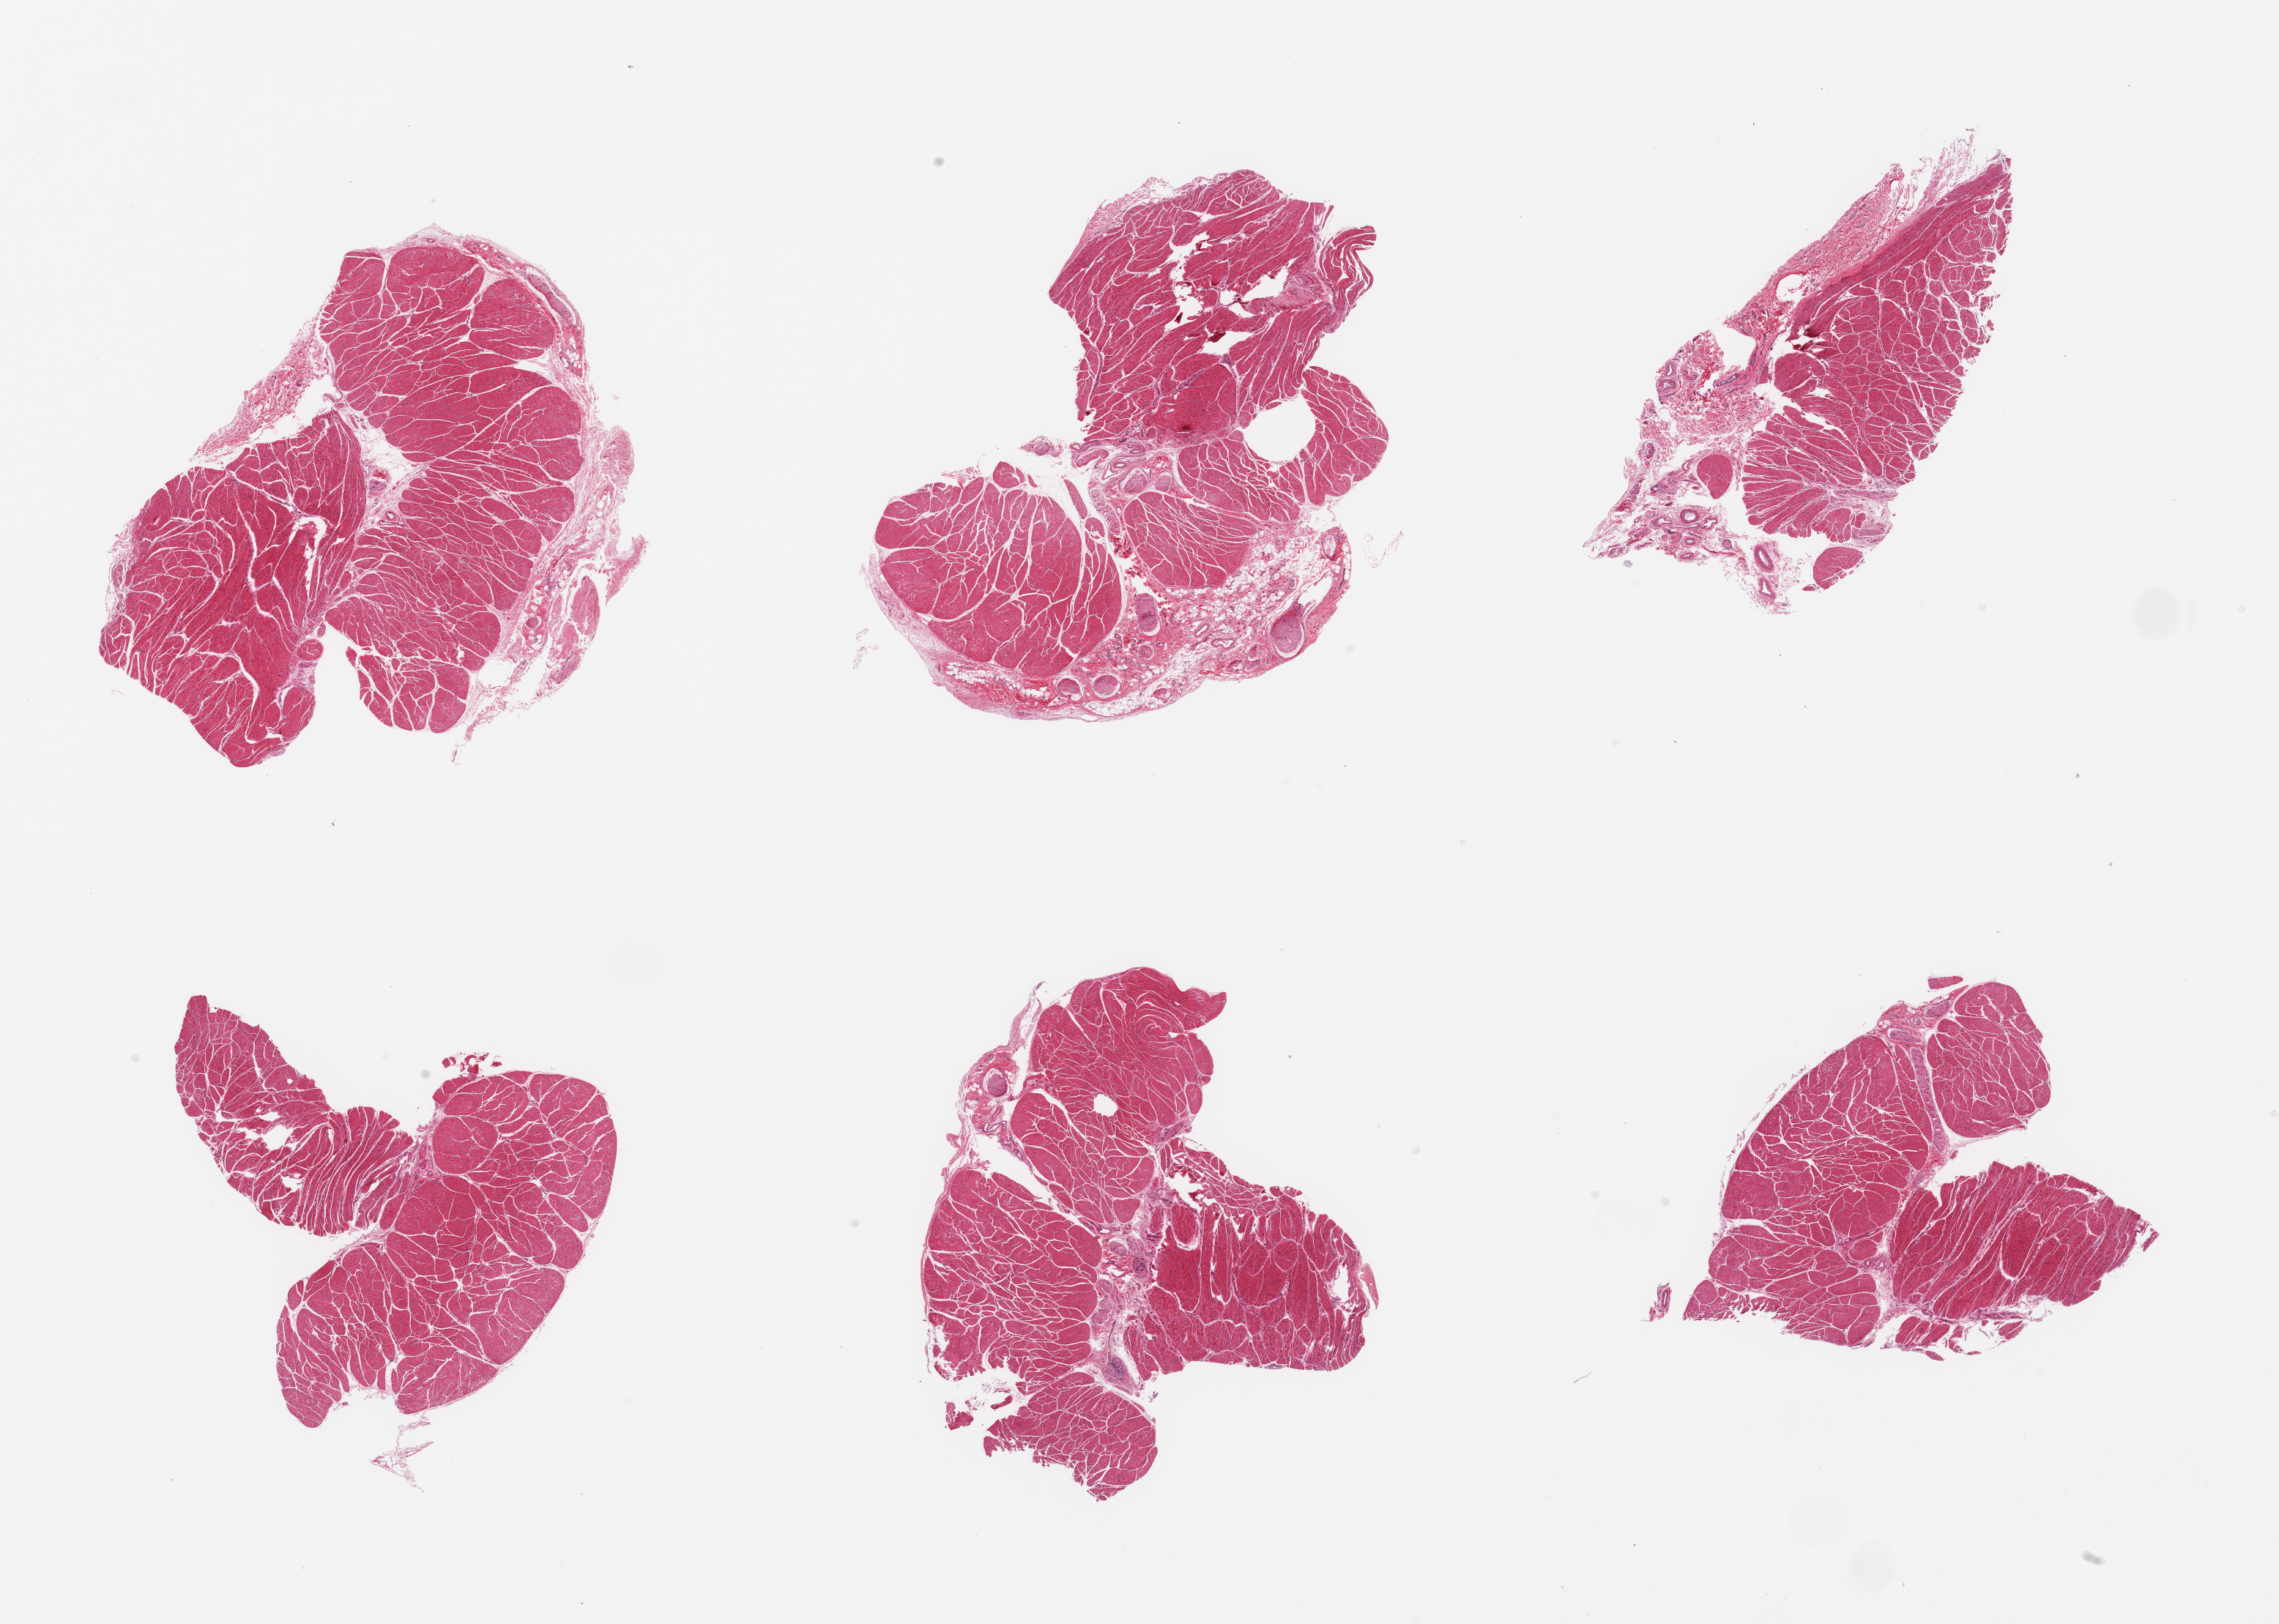
Hematoxylin and eosin (H&E) whole-slide image, brightfield, whole scanned area (about 24.6 x 17.5 mm) shown as a low-resolution overview. PAXgene-fixed paraffin-embedded (PFPE) section. Target tissue: esophageal muscle. Tissue donor sample. Donor: male.
Pathologist's review note for this sample: 6 pieces; target muscularis with some attached fat/vessels/nerve.